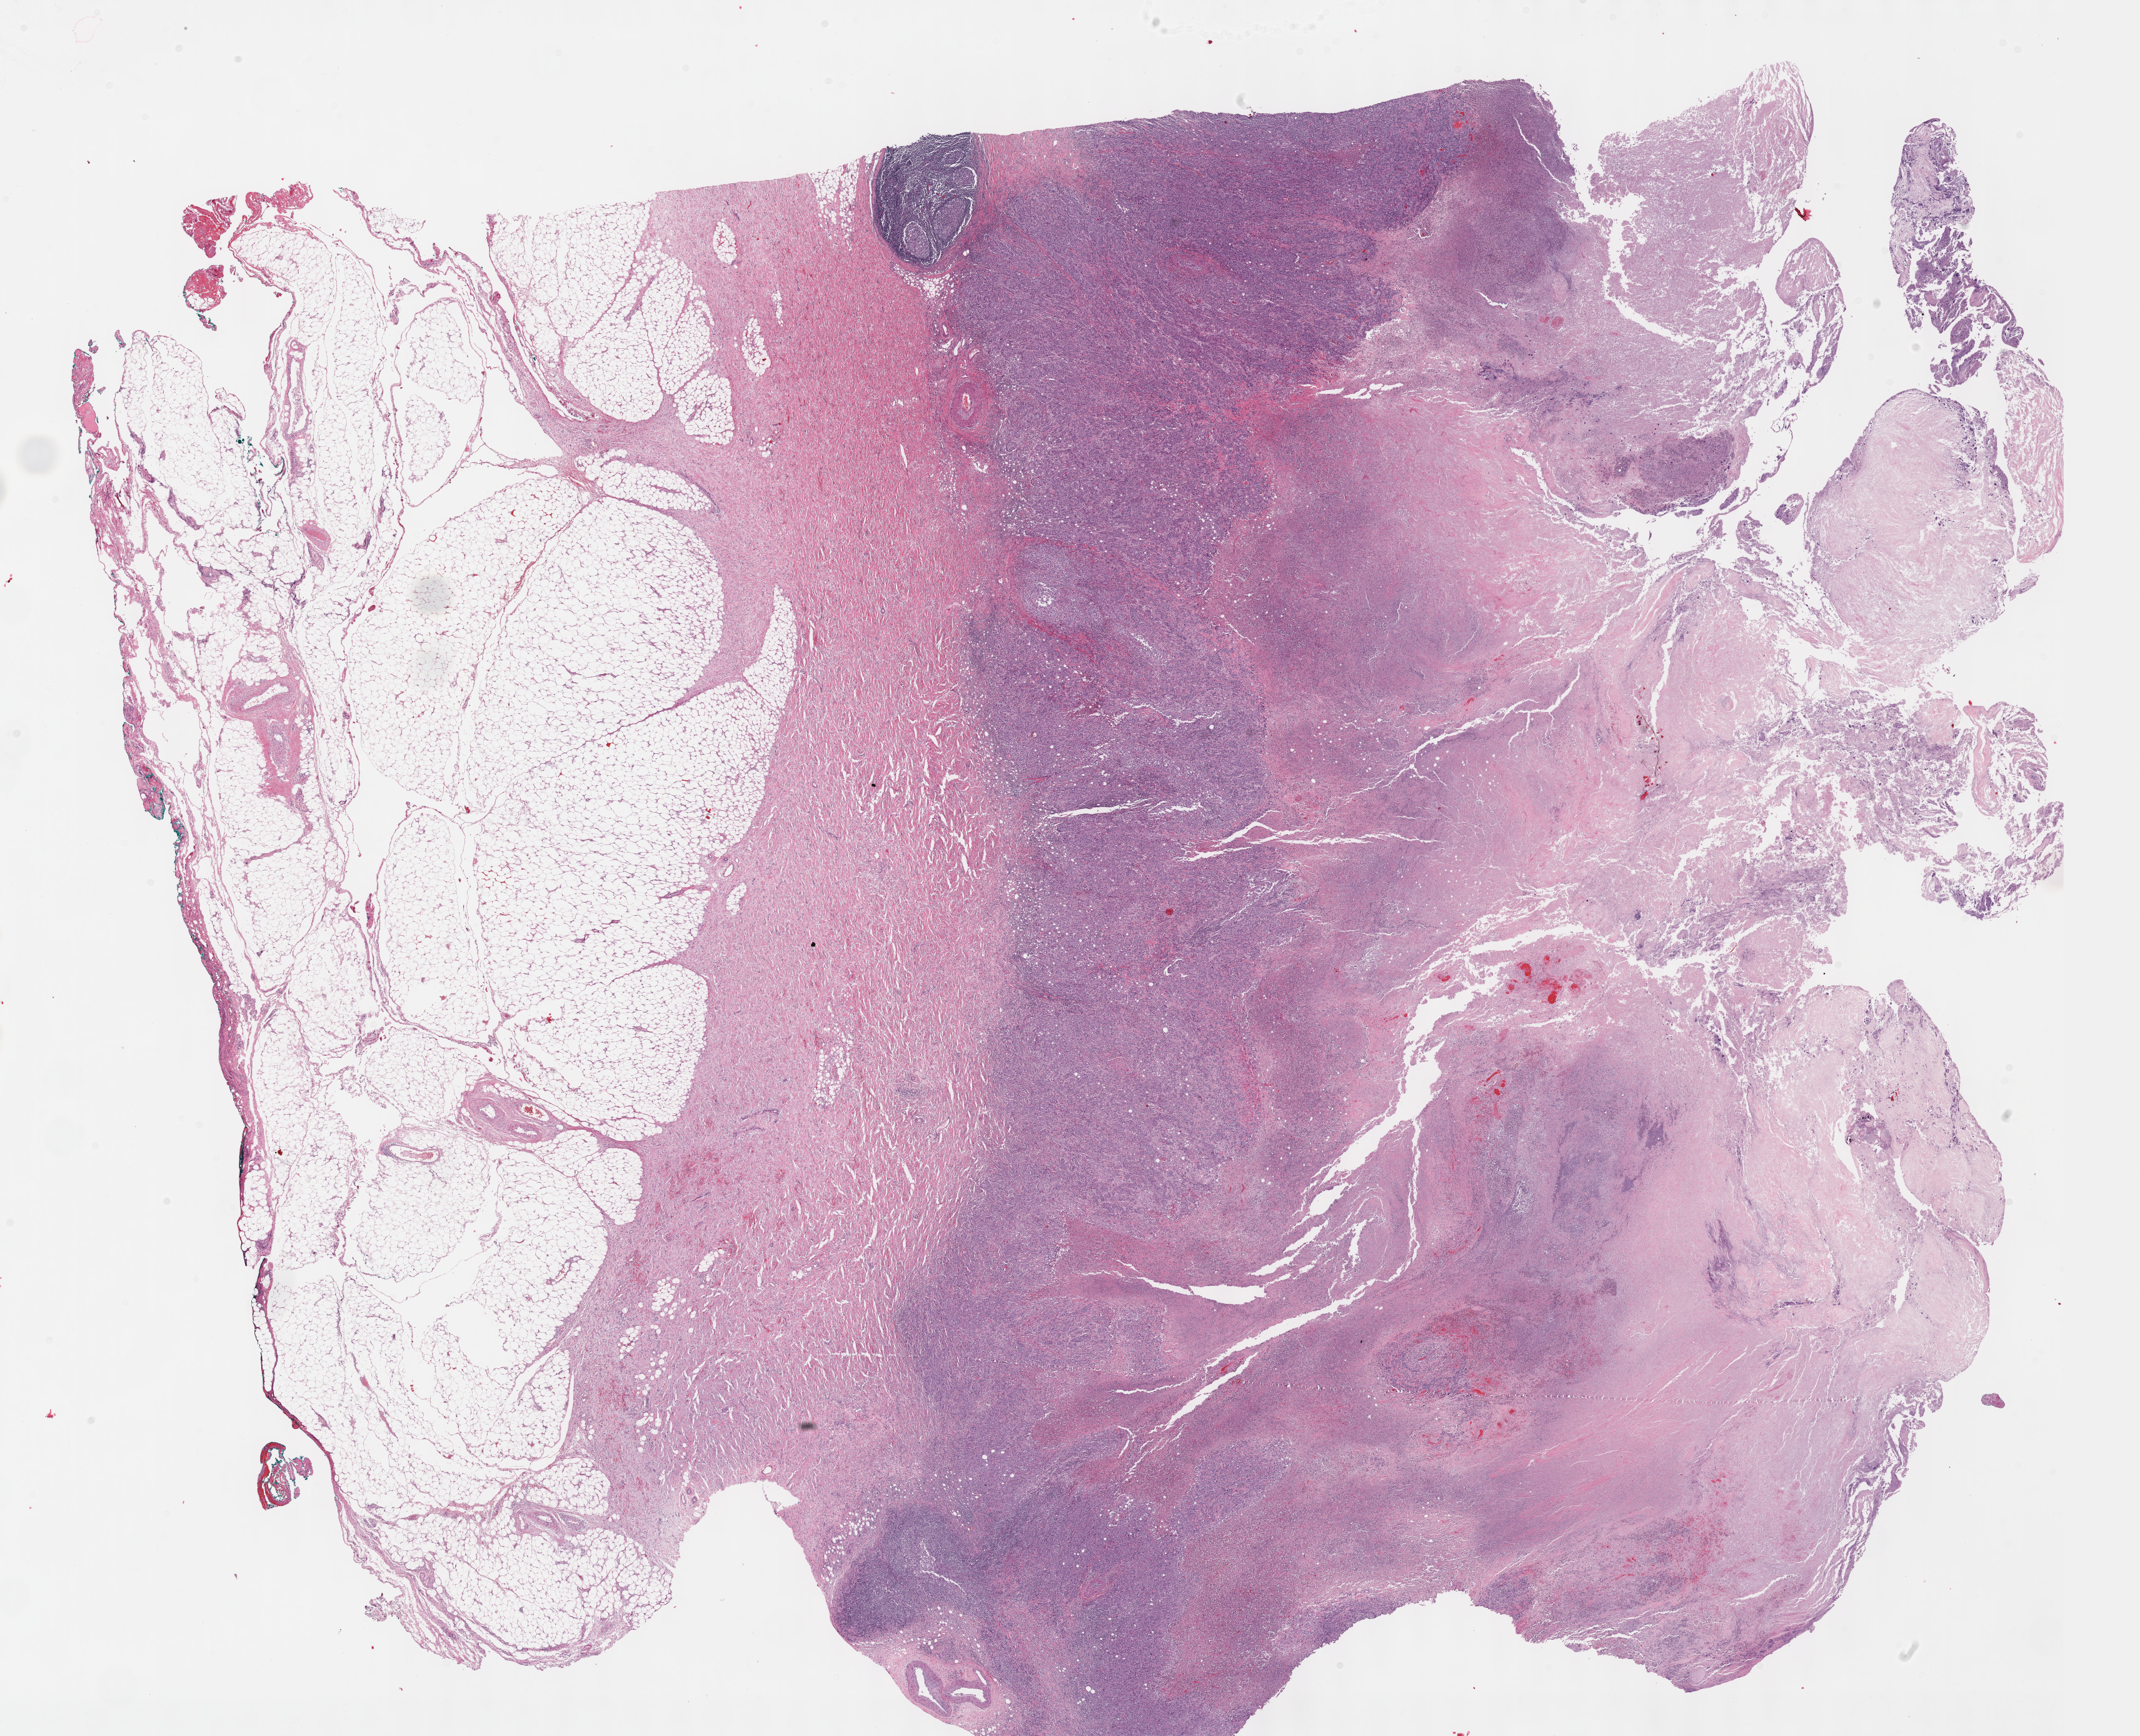
H&E whole-slide image, low-resolution overview of the scanned area, about 27.7 x 22.4 mm, formalin-fixed paraffin-embedded (FFPE) diagnostic section, sample: primary tumour, bladder. Male patient; age at initial diagnosis 87 years. Histologic grade: high grade.
Histologic diagnosis: Transitional cell carcinoma. AJCC pathologic stage: IV (7th edition).